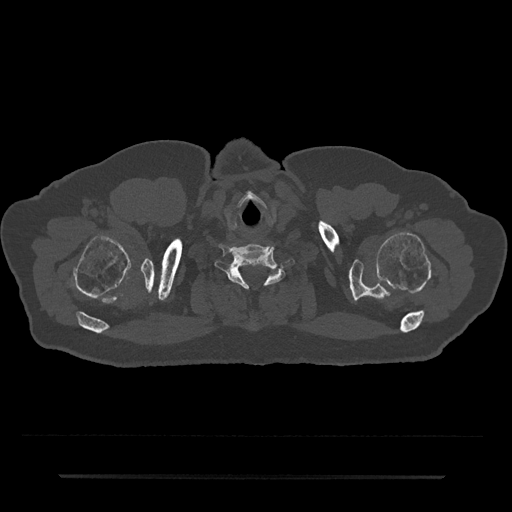
CT including the spine, one axial slice. Position 667 of 797 along the scan axis. Reconstruction kernel Br40s/3. 120 kVp. Bone window (W 1800 / L 400 HU). 0.5 mm slice thickness. 512 × 512 image matrix, field of view 437 × 437 mm. Male patient, age 69 years. Case-level facts recorded for this patient, not image findings: primary cancer: prostate.
Outlined on this slice (semi-automatically segmented with operator editing):
- T1 vertebra: bounding box <268,270,280,279> (left, top, right, bottom; pixels)